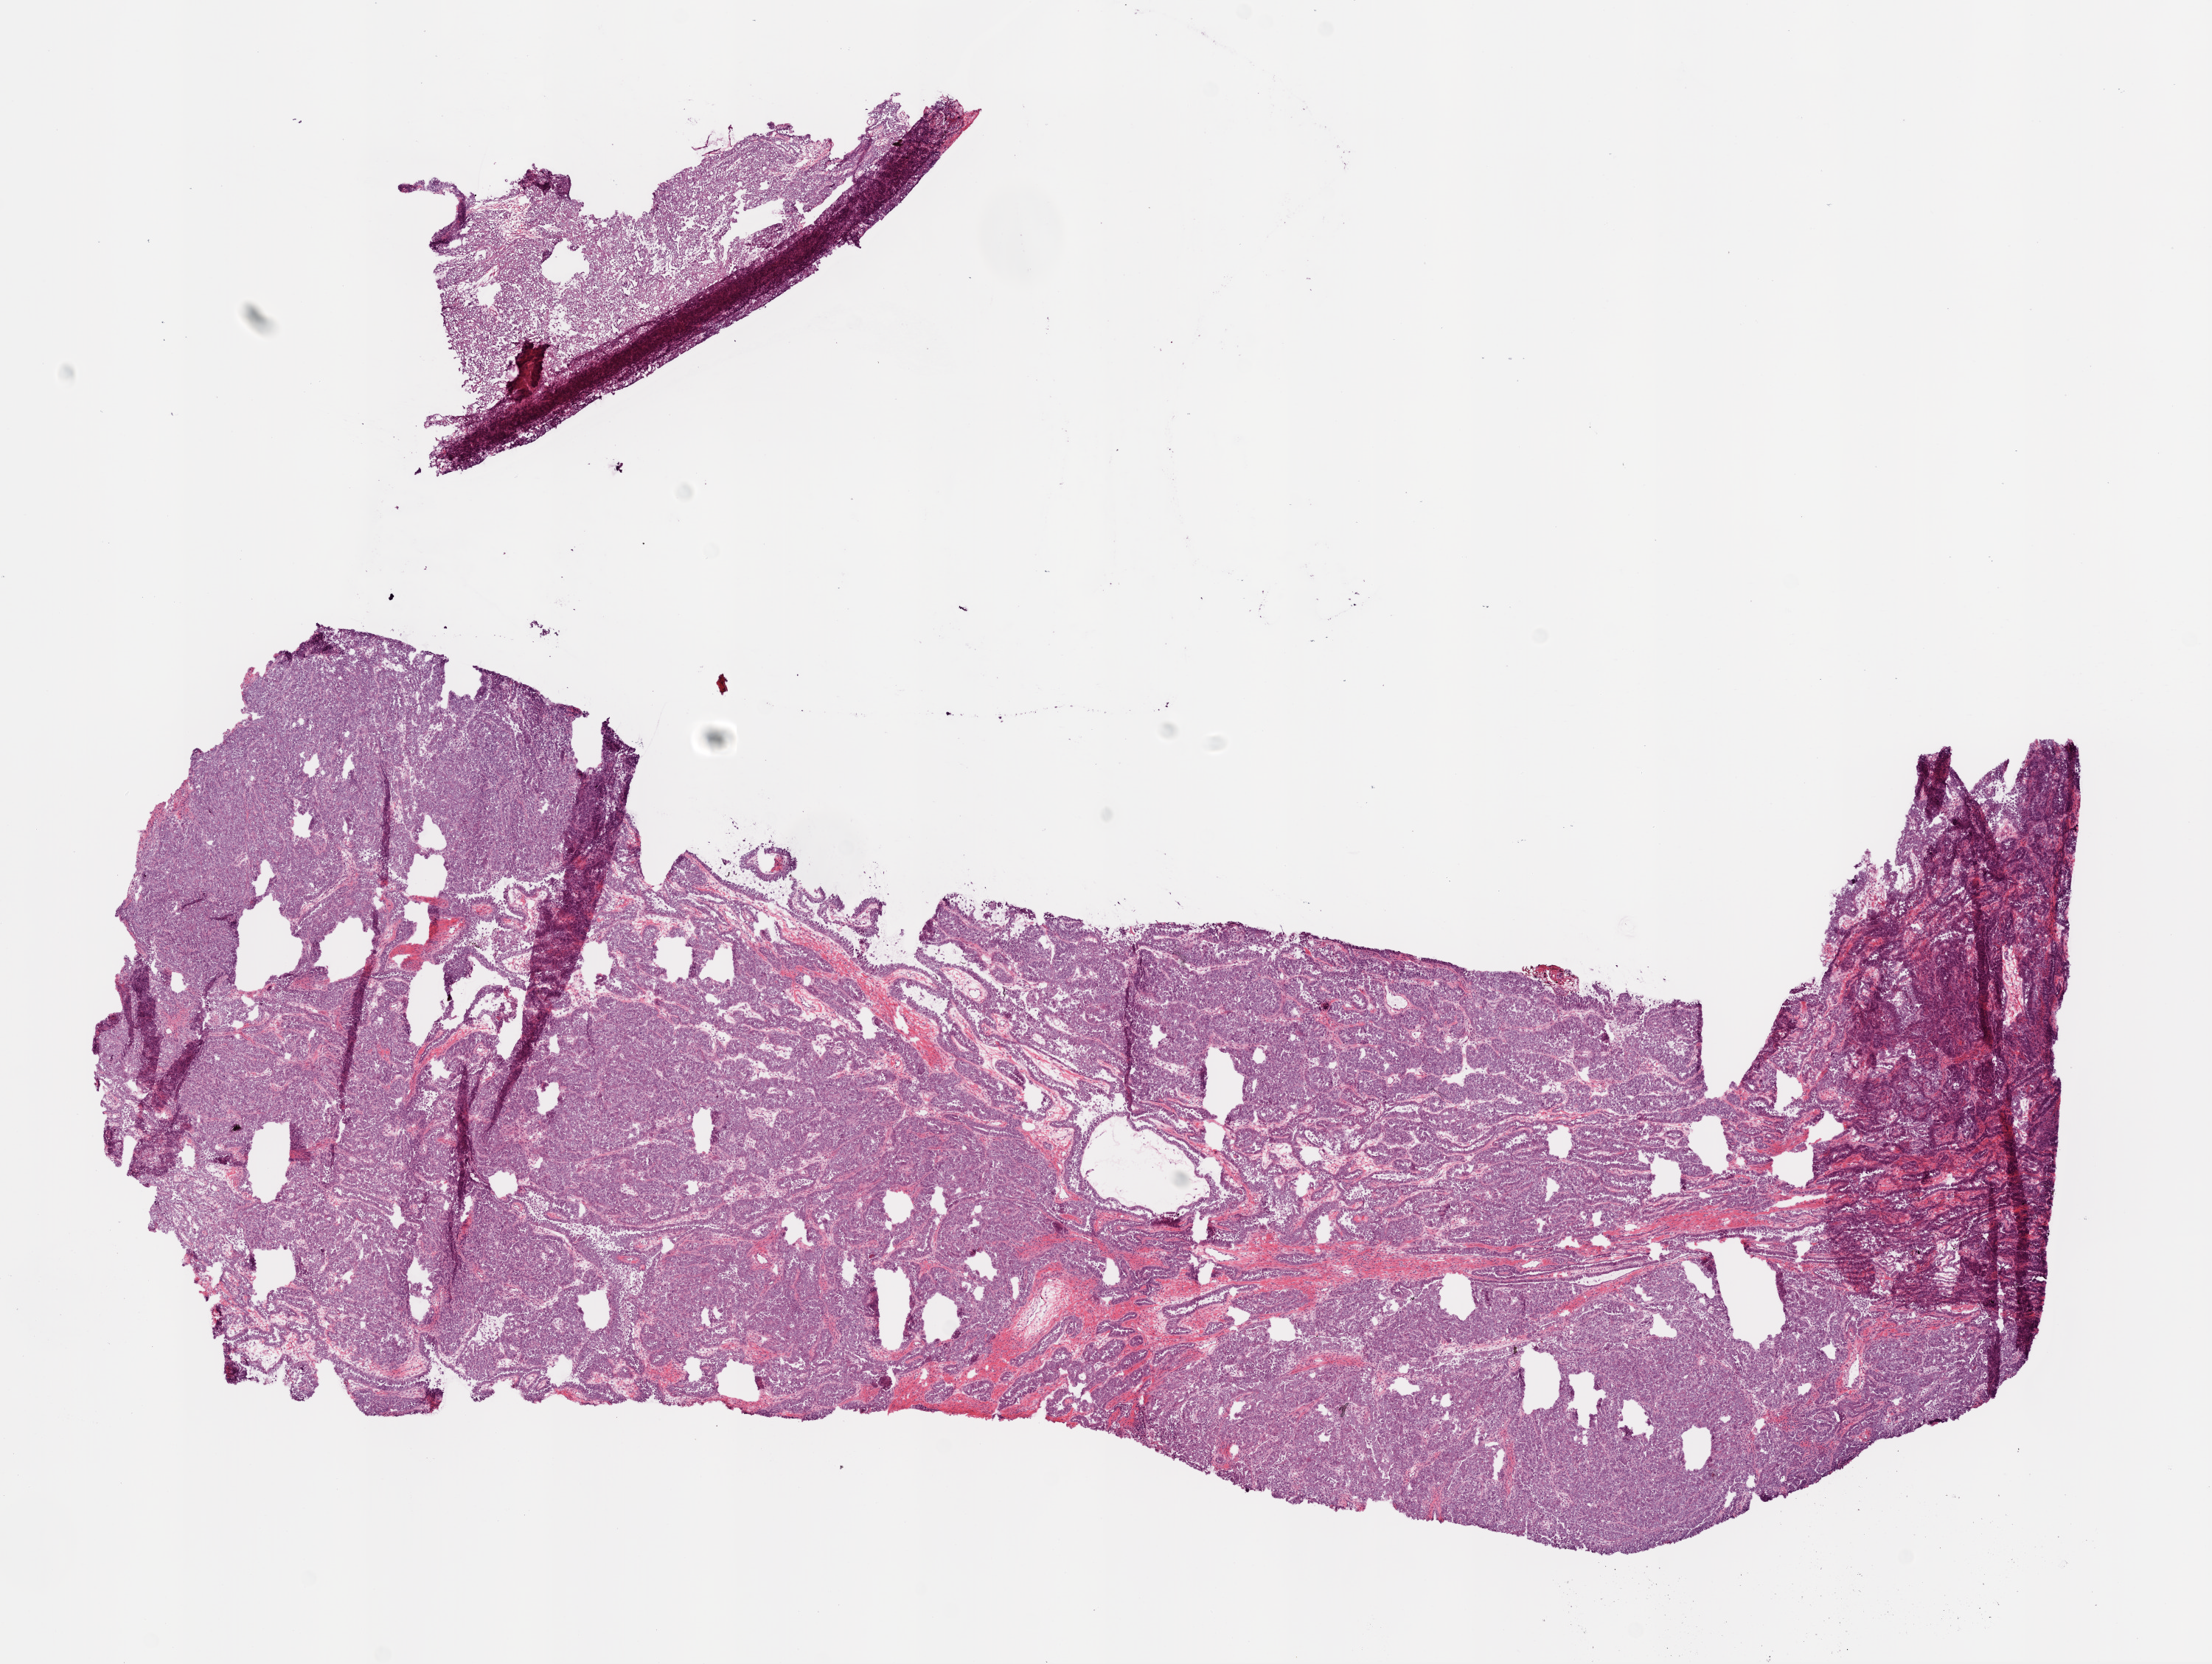
Whole-slide histology image, H&E, shown as a low-resolution overview of the whole scanned area (about 12.0 x 9.1 mm, from a 20x scan), frozen section from the bottom of the tissue portion, ovary, primary tumour sample. Patient: female, age at initial diagnosis 57 years. Histologic grade: G3 (poorly differentiated). Composition of this section per pathologist review: tumour cells 95%, tumour nuclei 99%, normal cells 0%, stromal cells 5%, necrosis 0%.
• FIGO stage: IIIA
• diagnosis: Serous cystadenocarcinoma, NOS